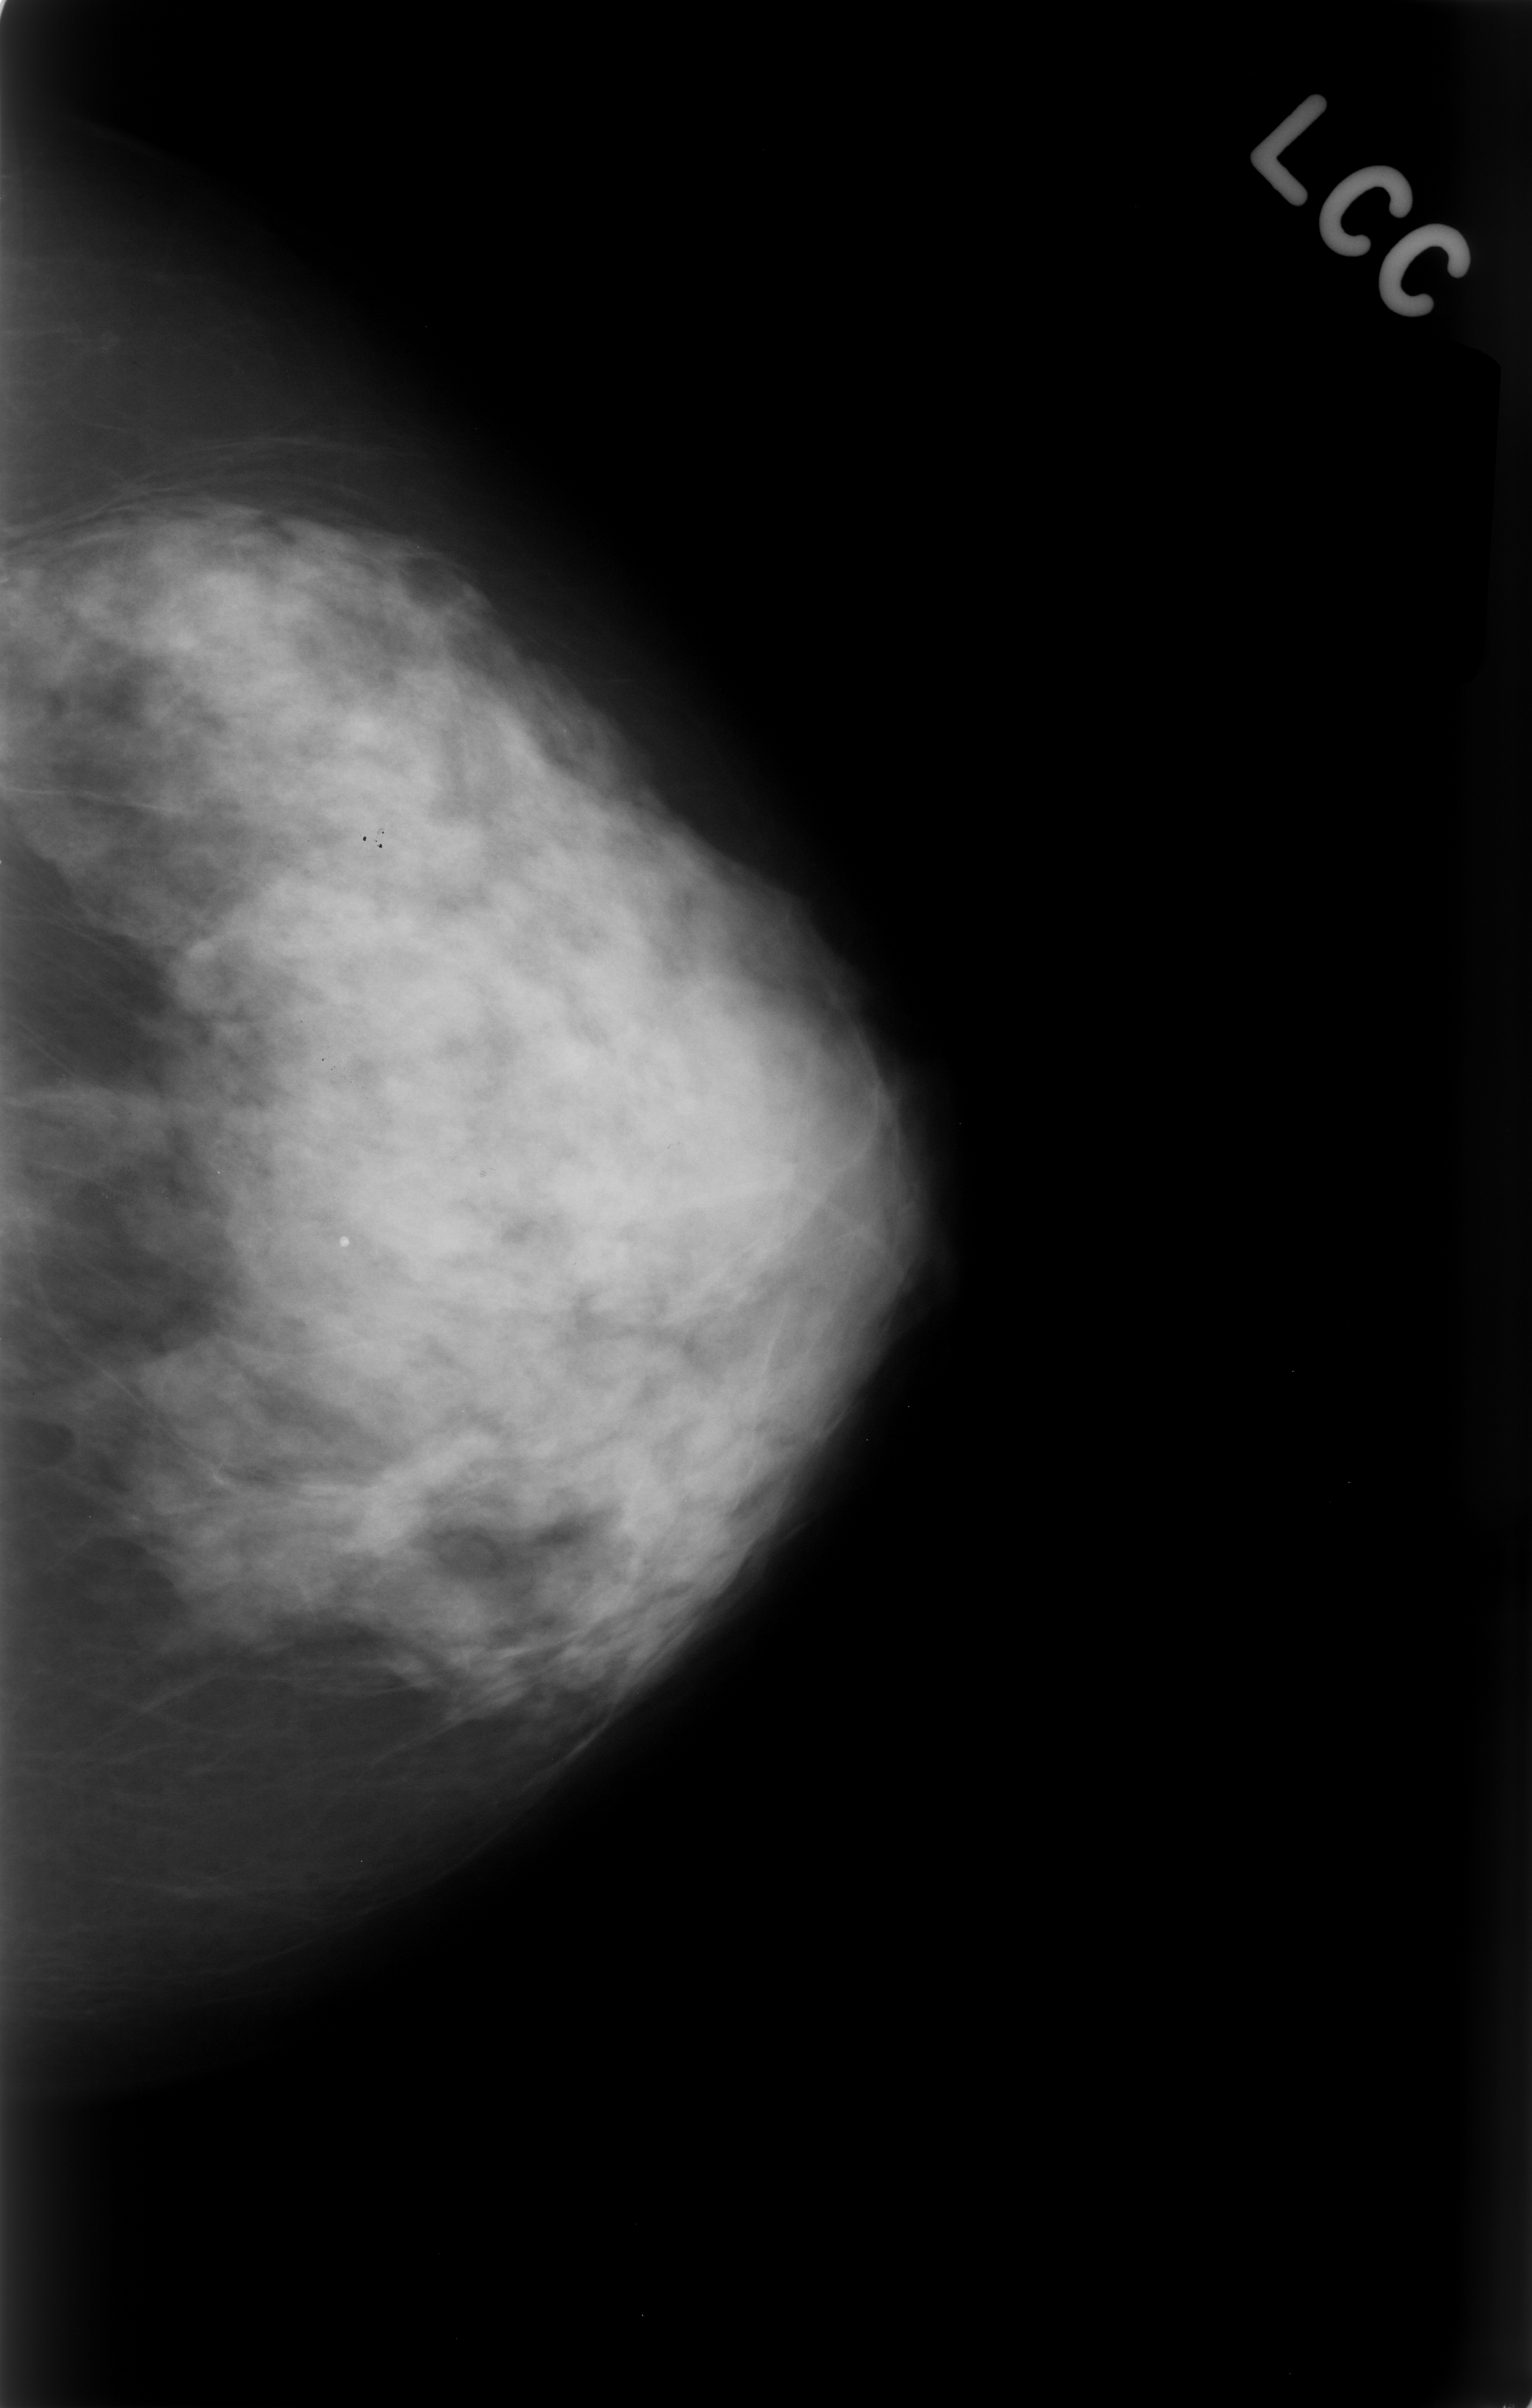
Scanned film-screen mammogram. Left breast. CC view. 1532 × 2408 image matrix.
Expert-marked regions of interest on this film, with their recorded descriptors:
- calcifications, morphology amorphous, distribution segmental; BI-RADS assessment category 4; pathology (as recorded): benign: bounding box [x1, y1, x2, y2] px = [0, 1111, 359, 1340]